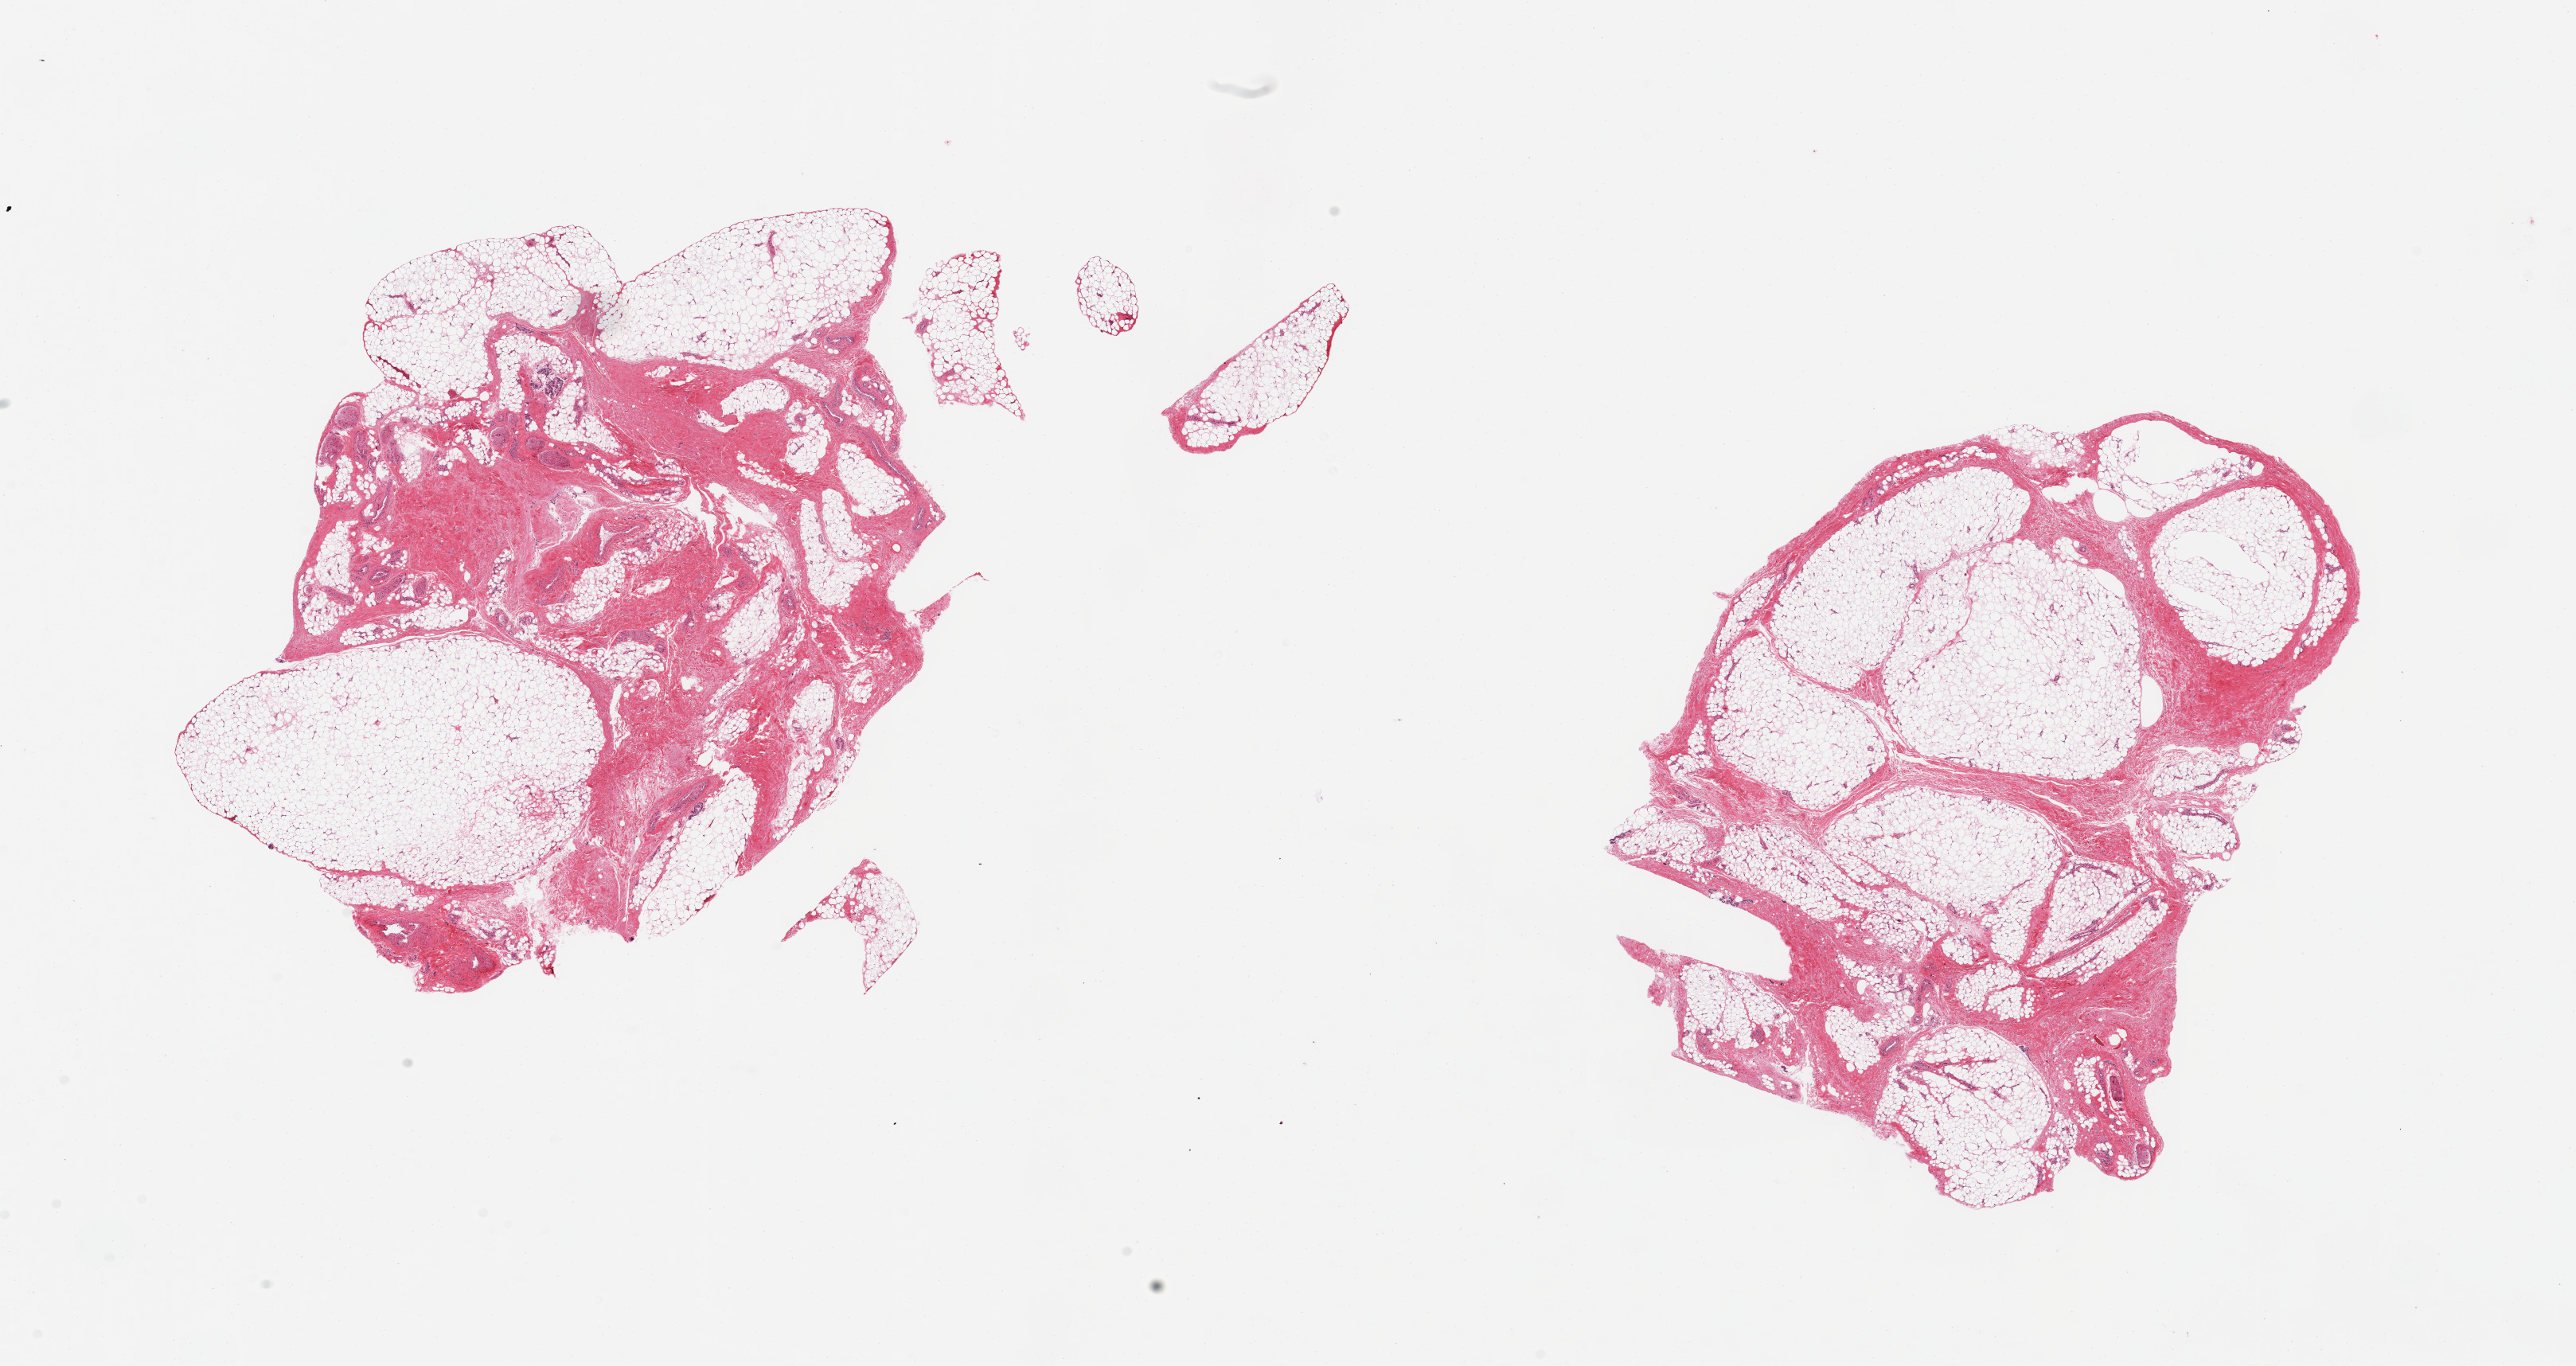
Whole-slide image, hematoxylin and eosin (H&E) stain, a low-resolution overview of the entire scanned area, about 25.6 x 13.6 mm (from a 20x scan). PAXgene-fixed, paraffin-embedded tissue. Target tissue: adipose tissue. Tissue donor sample.
• reviewer comment on this tissue sample: 2 pieces; 20 & 40% fibrovascular content; small [0.3mm] focus of glandular carry-over